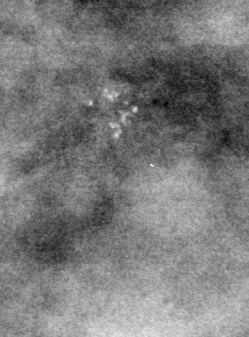
Region of interest cut from a scanned film mammogram (one marked finding), left breast, MLO view, BI-RADS breast density category 4 (scale 1–4).
- Marked abnormality: calcifications, morphology pleomorphic, distribution clustered; BI-RADS assessment category 4; pathology result (as recorded, not read from the image): benign.